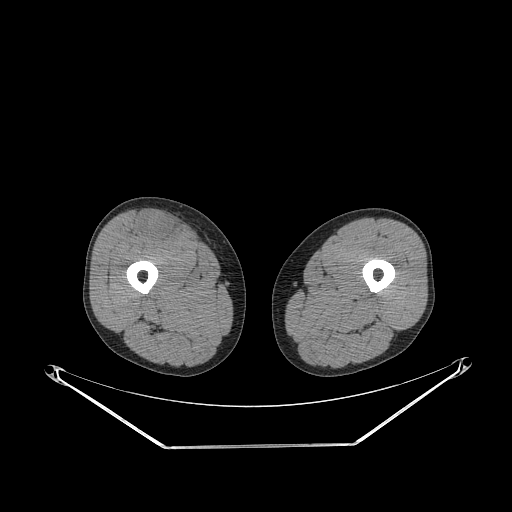
CT of an extremity soft-tissue mass (from a PET/CT study), one axial slice. Position 255 of 311 along the scan axis. Soft-tissue window (W 400 / L 40 HU). 512 × 512 image matrix. Male patient. From the clinical record (not read from this slice): histological type: pleiomorphic leiomyosarcoma; grade: intermediate; site of the primary tumour: right thigh.
Annotated regions visible in this slice (expert contour drawn on MRI and transferred to this co-registered scan by the dataset authors):
- gross tumour volume including surrounding oedema: bounding box <139,212,182,243> (left, top, right, bottom; pixels)